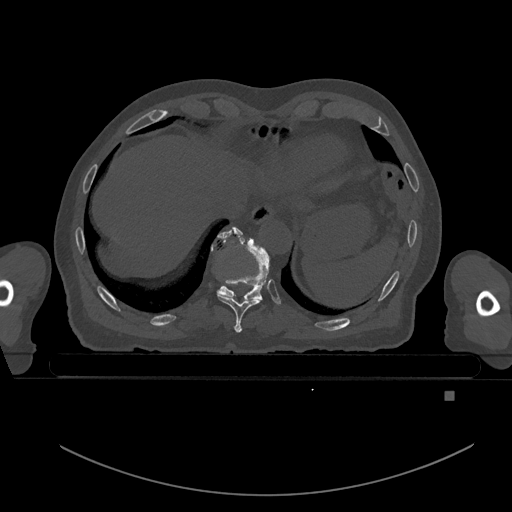
CT including the spine, one axial slice. Position 121 of 969 along the scan axis. Bone window (W 1800 / L 400 HU). 0.5 mm slice thickness. 512 × 512 image matrix. Patient: male, 82 years. Case-level facts recorded for this patient, not image findings: primary cancer: prostate; vertebrae with lytic lesions (as recorded): T11, T9, T8, T2.
Outlined on this slice (semi-automatically segmented with operator editing):
- T10 vertebra: bounding box <212,226,270,300> (left, top, right, bottom; pixels)
- T9 vertebra: <216,230,262,333>